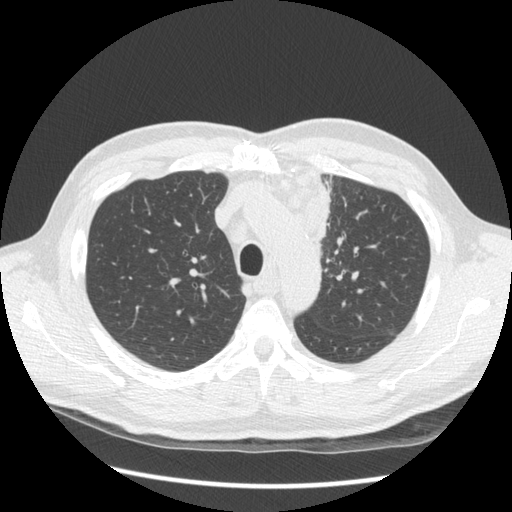
Low-dose screening chest CT, one axial slice; slice 105 of 136 in the series (ordered by position); 120 kVp; lung window (W 1500 / L -600 HU); 512 × 512 image matrix.
Structures marked on this image (manually delineated by an expert):
- lesion 1 (tumor, upper lobe of left lung): bounding box (x1, y1, x2, y2) in pixels: (279, 167, 331, 246)